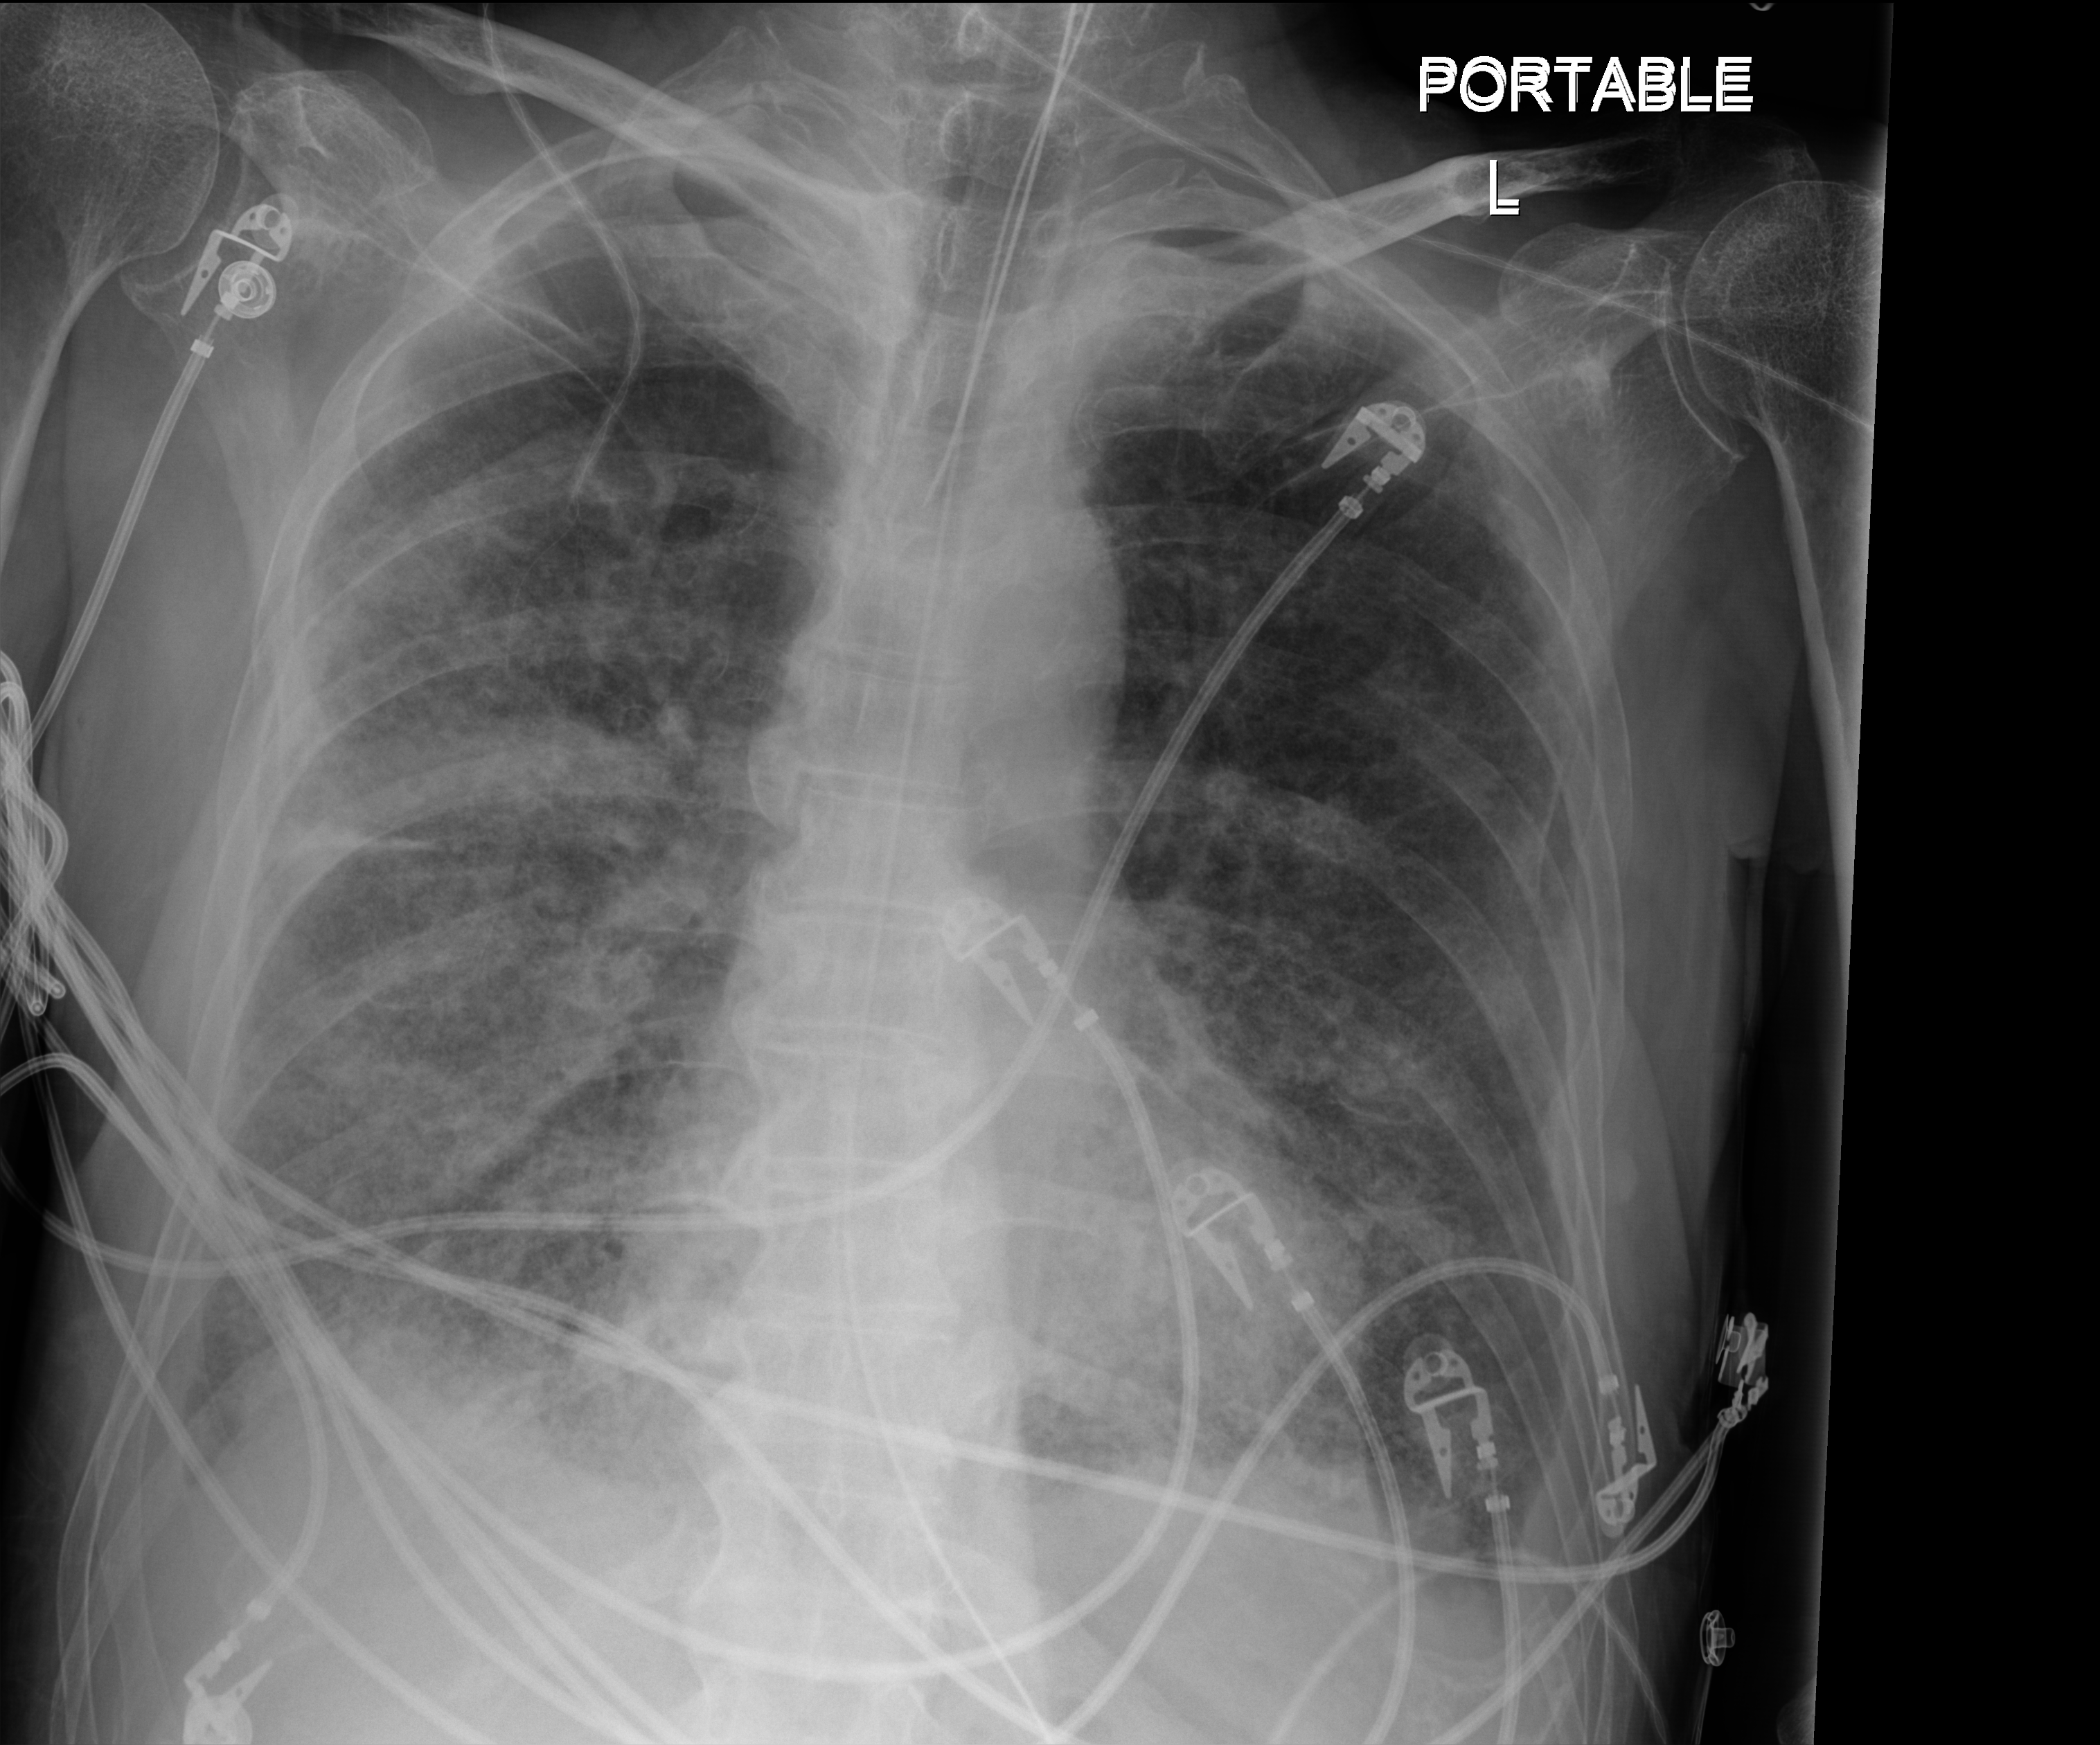
Chest X-ray (portable). Patient hospitalised with COVID-19; male, aged 60–74 years.
Admission-level facts for this patient (not findings on this image; timing relative to this image not recorded):
- length of hospital stay: 42 days